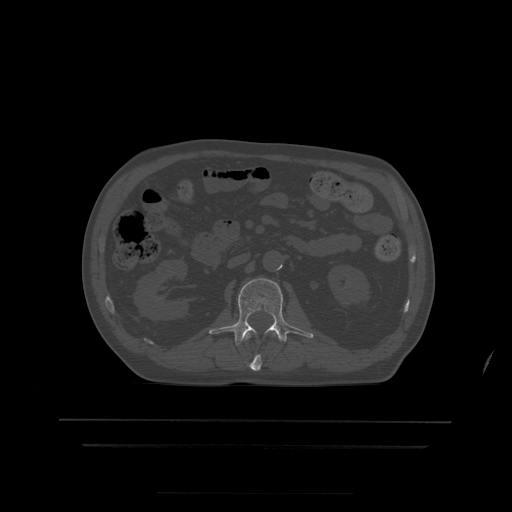
CT including the spine, one axial slice. Slice 150 of 522 in the series (ordered by position). Bone window (W 1800 / L 400 HU). 1.25 mm slice thickness. 512 × 512 image matrix, field of view 436 × 436 mm. Patient age 68 years. Case-level facts recorded for this patient, not image findings: primary cancer: urothelial.
Annotated regions visible in this slice (semi-automatic segmentation, software-assisted and operator-edited):
- L1 vertebra: box from (x=244, y=333) to (x=278, y=372) px
- L2 vertebra: (x=209, y=278)–(x=314, y=346)